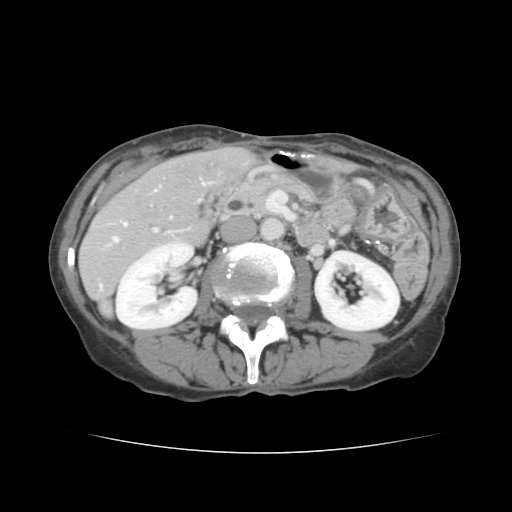
Contrast-enhanced abdominal CT, one axial slice. Position 57 of 136 along the scan axis. 120 kVp. Intravenous contrast given. Soft-tissue window (W 400 / L 40 HU). 2.5 mm slice thickness. 512 × 512 image matrix, field of view 319 × 319 mm. Female patient, age 77 years. Case-level facts recorded for this patient, not image findings: diagnosis: colorectal cancer liver metastases, imaged before liver resection; multiple liver metastases: yes; largest metastasis: 3 cm; disease in both lobes: no.
Outlined on this slice (expert manual segmentation):
- hepatic veins: bounding box [x1, y1, x2, y2] px = [113, 182, 205, 242]
- liver: [80, 146, 254, 312]
- planned liver remnant (the part of the liver to remain after resection): [166, 146, 254, 197]
- portal vein (with intrahepatic branches): [100, 182, 211, 288]